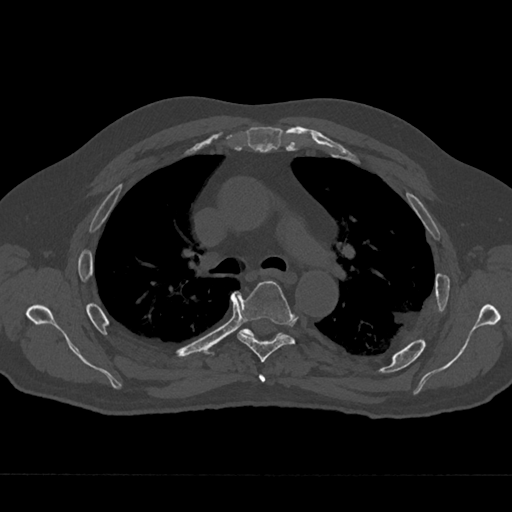
CT including the spine, one axial slice. Position 465 of 797 along the scan axis. Reconstruction kernel Br40s/3. 120 kVp. Bone window (W 1800 / L 400 HU). 512 × 512 image matrix. Patient: male, 75 years. Case-level facts recorded for this patient, not image findings: primary cancer: renal.
Structures marked on this image (semi-automatically segmented with operator editing):
- T4 vertebra: bounding box [x1, y1, x2, y2] px = [259, 374, 266, 382]
- T5 vertebra: [237, 281, 295, 362]
- T6 vertebra: [240, 328, 280, 337]